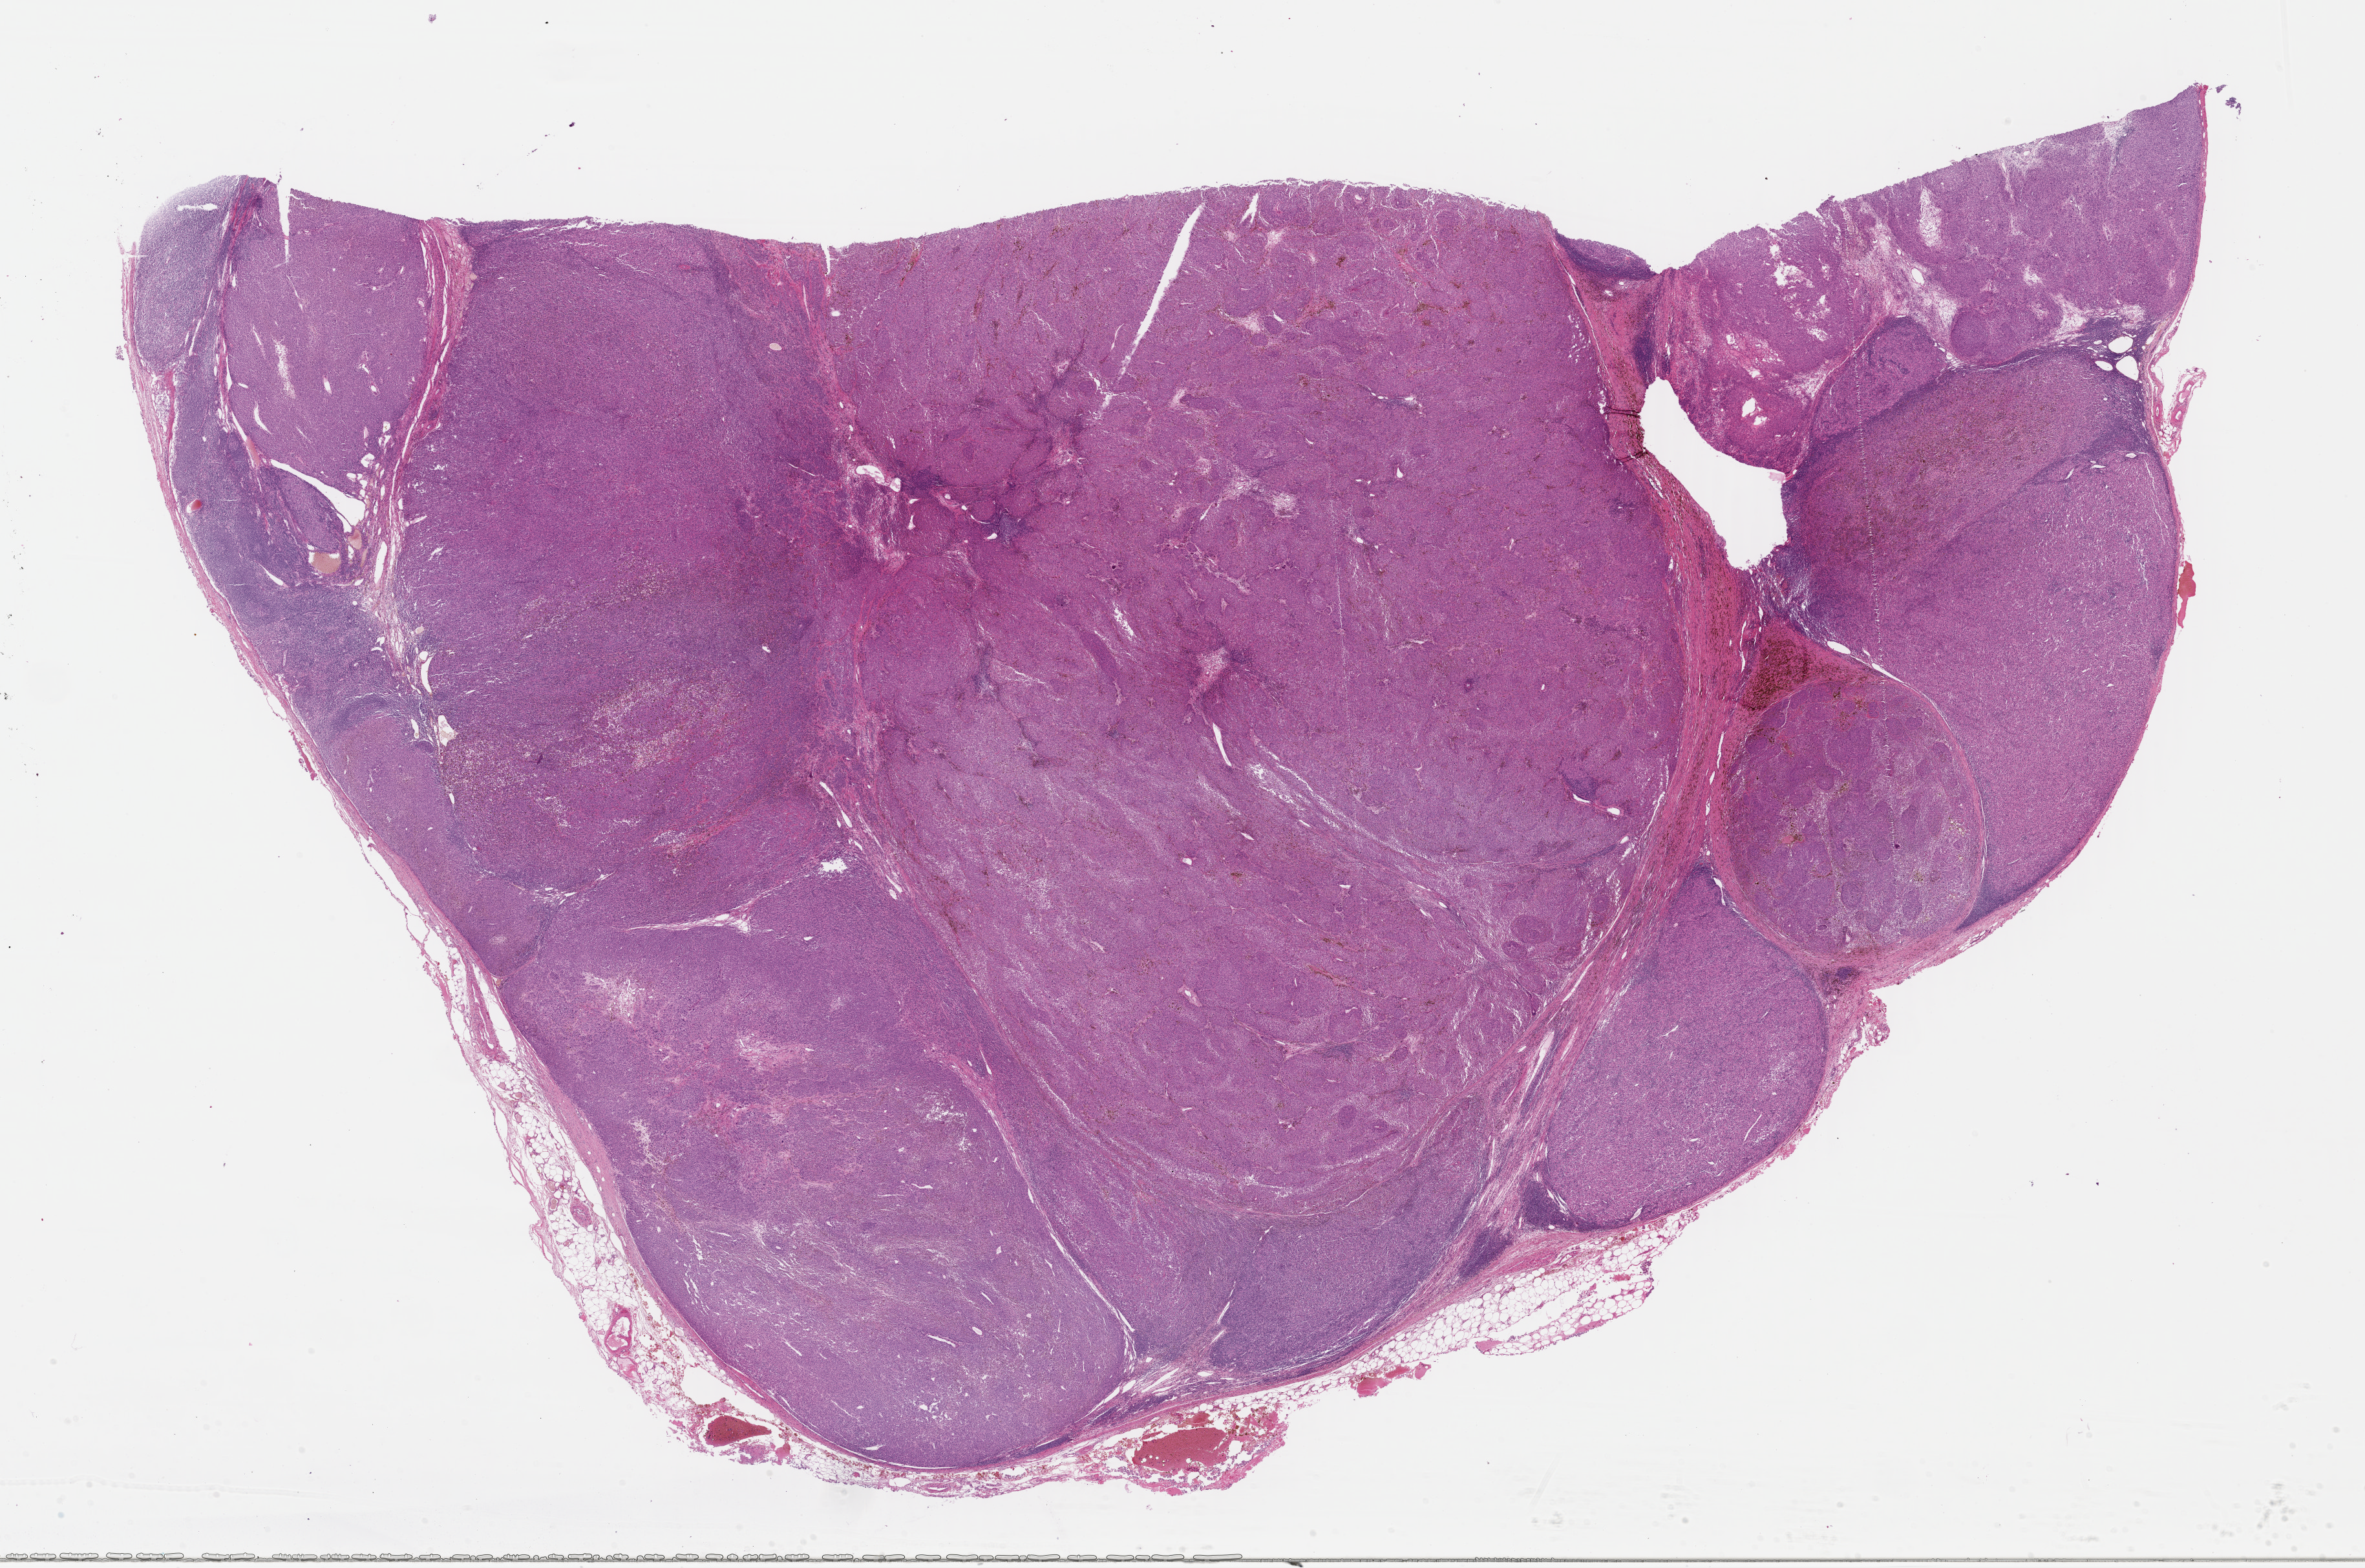
Whole-slide histology image, Hematoxylin and eosin (H&E) stained, a low-resolution overview of the entire scanned area, about 28.8 x 19.1 mm (acquisition: 40x scan); FFPE section; sample: primary tumour, skin. Patient: male, age at initial diagnosis 58 years.
Diagnosis: Malignant melanoma, NOS.